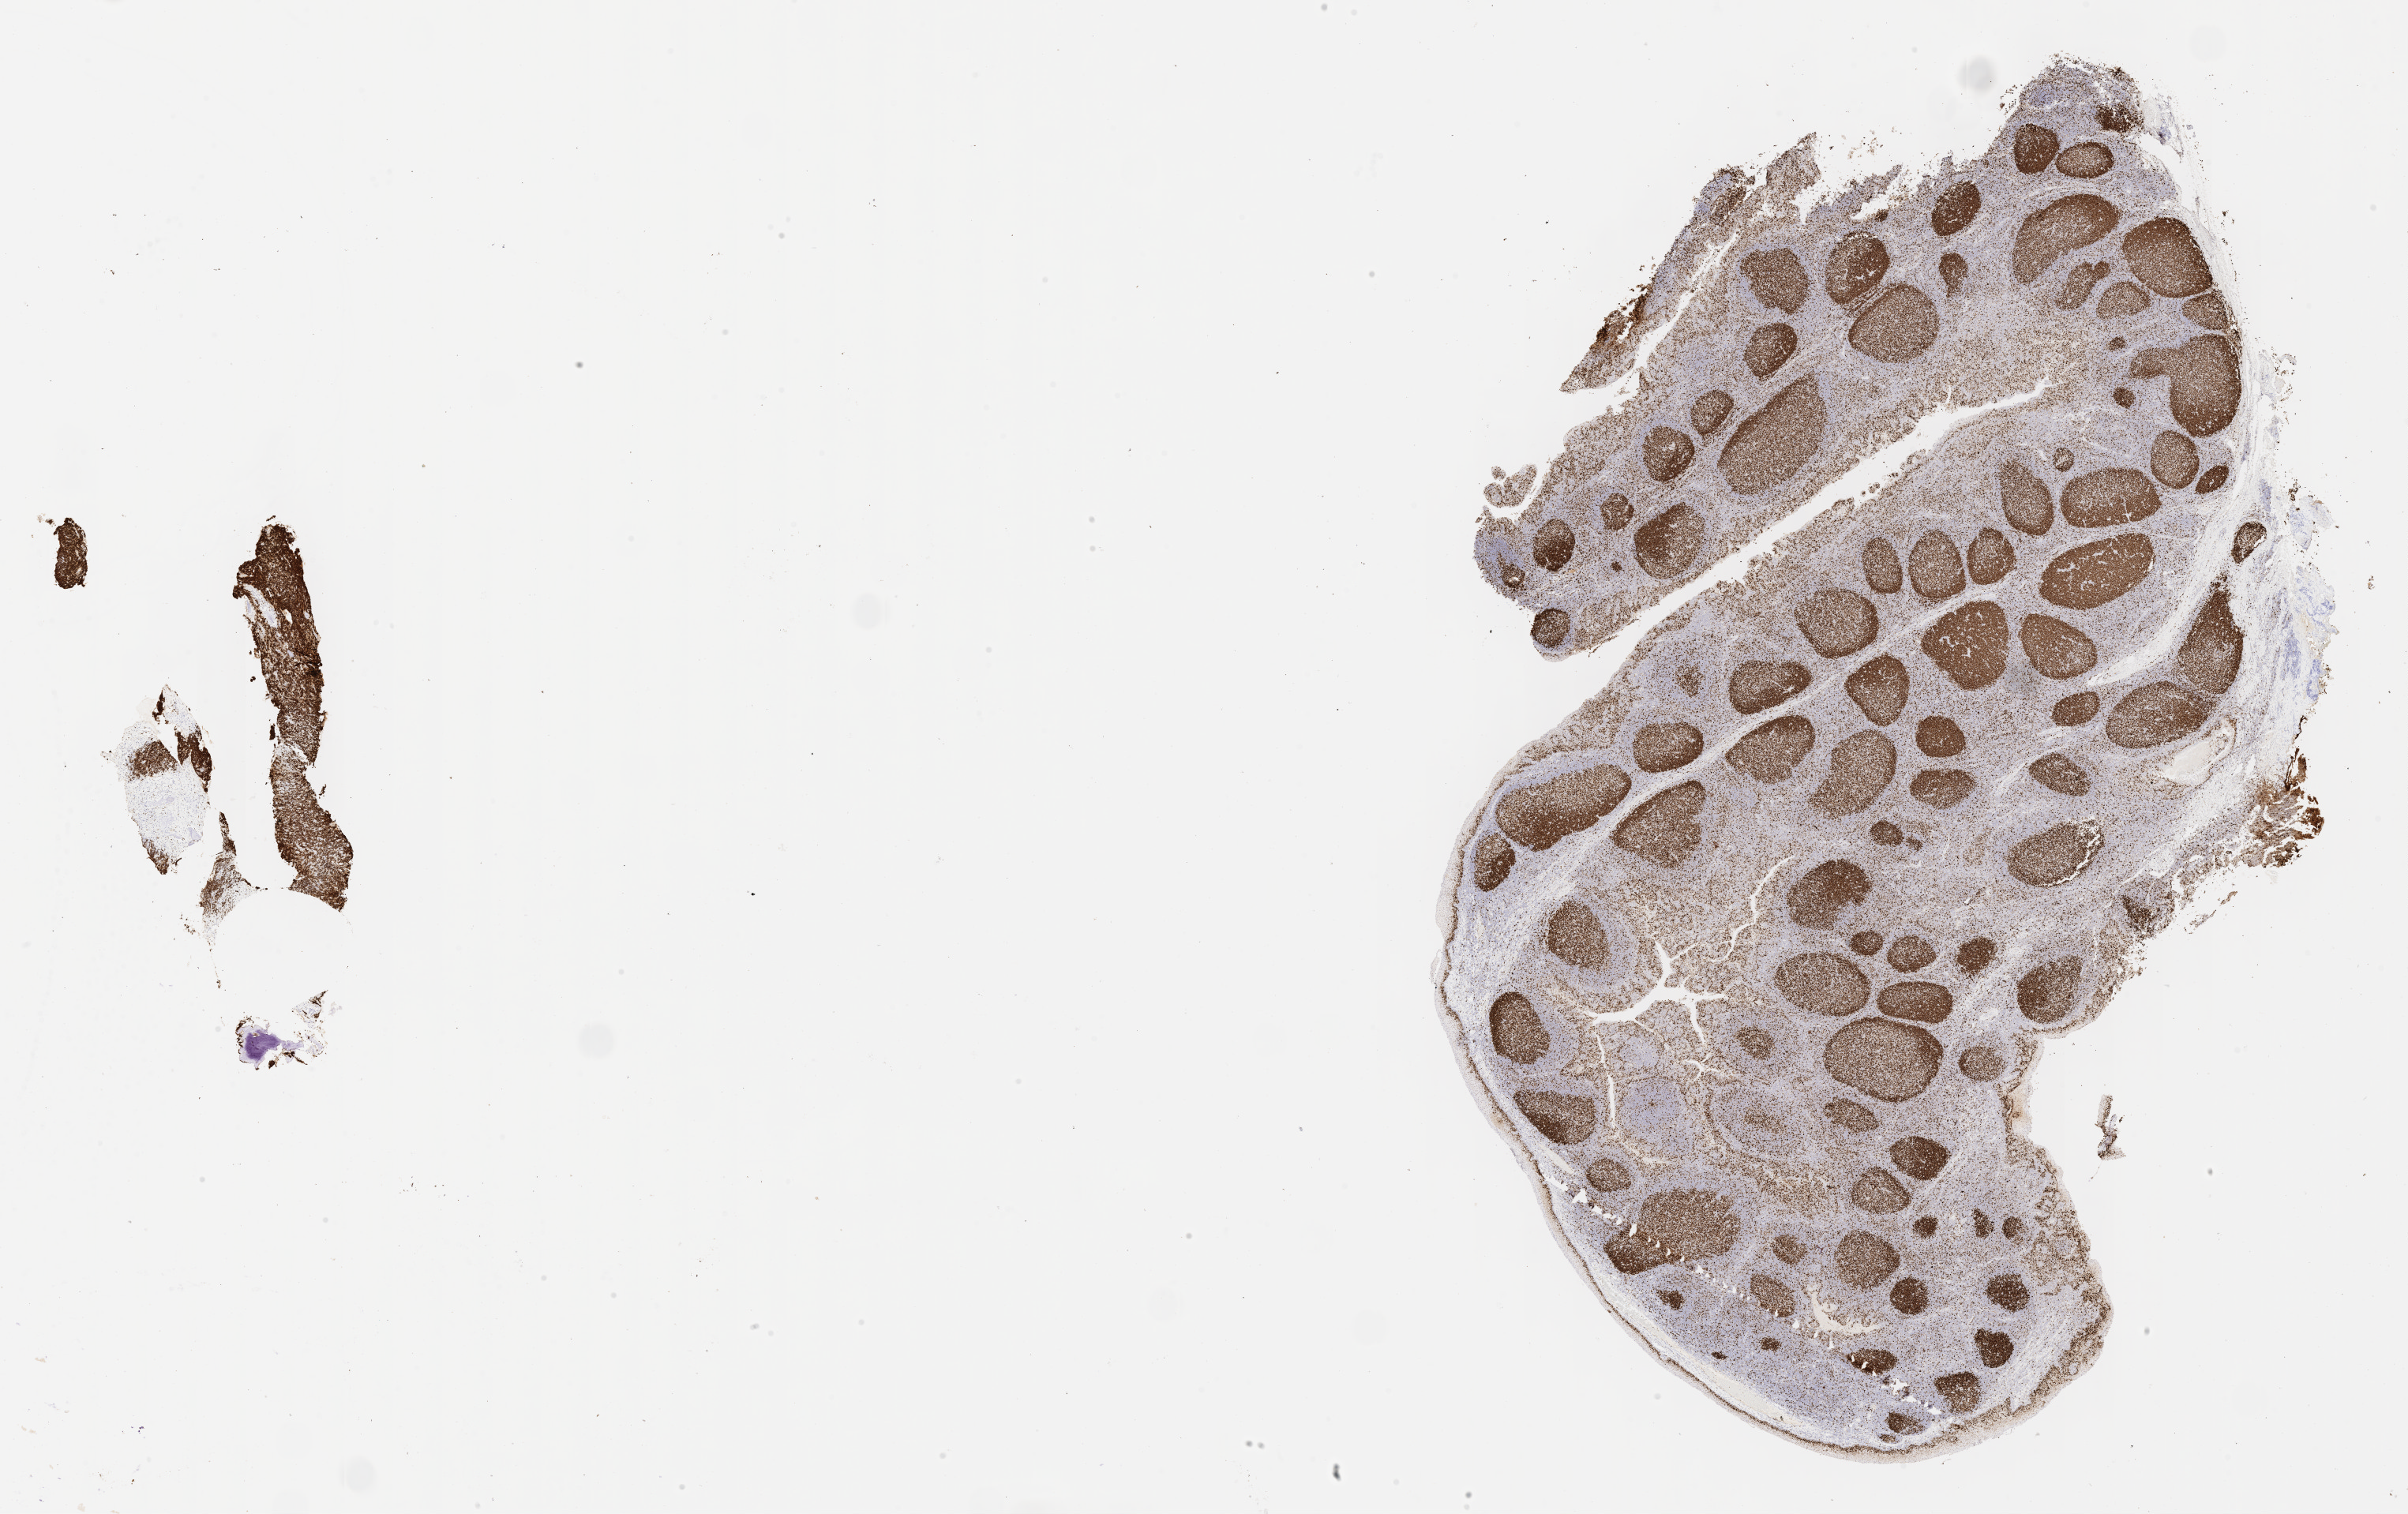
IHC for Ki-67, whole-slide image — shown as a low-resolution overview of the whole scanned area (about 24.7 x 15.5 mm). Specimen: tumor tissue. Site: mandible. Patient: male, age at initial diagnosis 6 years.
- diagnosis: Burkitt lymphoma, NOS